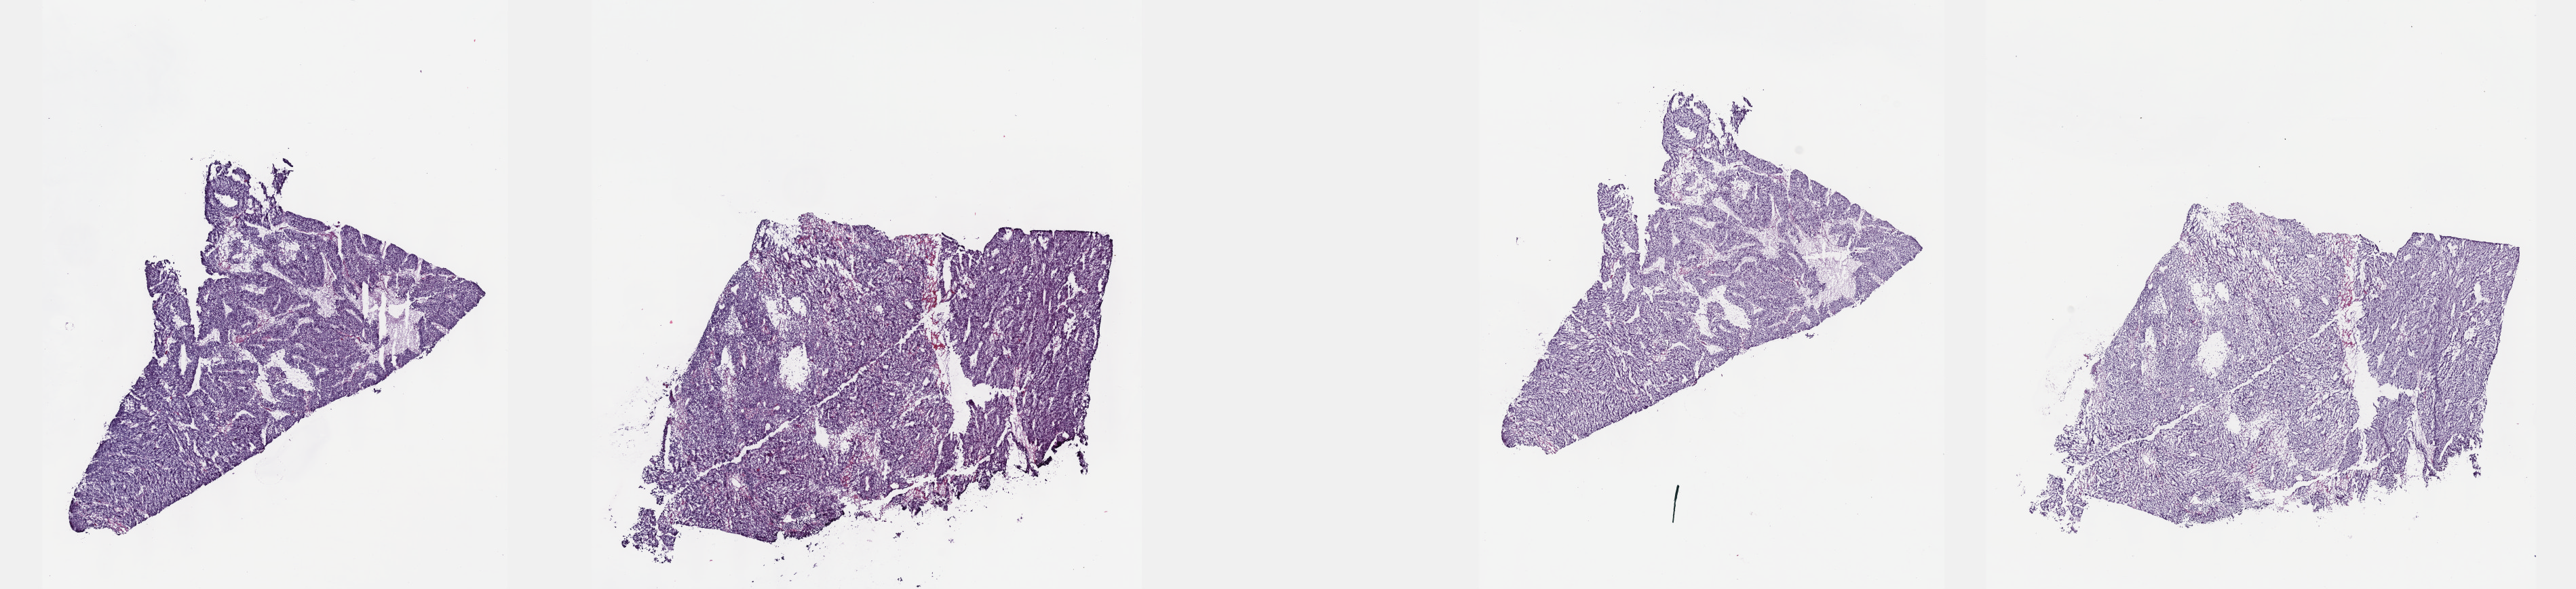
Digitized H&E tissue section (whole slide) — a low-resolution overview of the entire scanned area, about 30.7 x 7.0 mm (acquisition: 40x scan); frozen section from the top of the tissue portion; primary tumour sample from the liver. Female patient; age at initial diagnosis 64 years. Histologic grade: G3 (poorly differentiated). Slide review estimates, as recorded: tumour cells 100%, tumour nuclei 93%, normal cells 0%, stromal cells 0%, necrosis 0%. Infiltration values recorded for this section: lymphocyte infiltration 0%, monocyte infiltration 0%, neutrophil infiltration 0%.
* diagnosis: Hepatocellular carcinoma, NOS
* AJCC pathologic stage: II